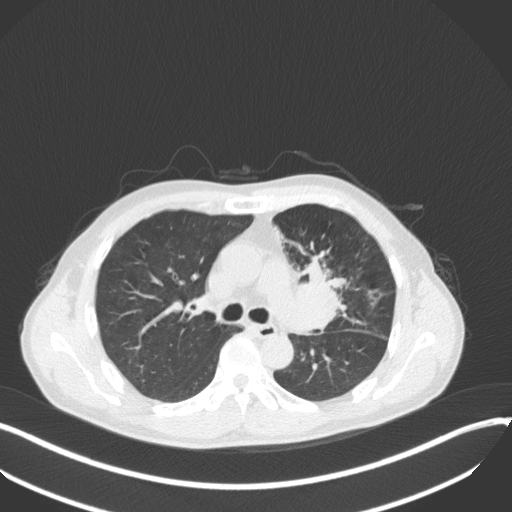
Chest CT, one axial slice; slice 215 of 411 in the series (ordered by position); reconstruction kernel B31f; 120 kVp; lung window (W 1500 / L -600 HU); 512 × 512 image matrix, field of view 400 × 400 mm. Male patient, age 56 years. From the clinical record (not read from this slice): clinical TNM (as recorded): T2a N0 M0.
Annotated regions visible in this slice (rectangle marked by the reading radiologist):
- lung tumour (recorded histology: squamous cell carcinoma): bounding box [x1, y1, x2, y2] px = [292, 248, 346, 343]